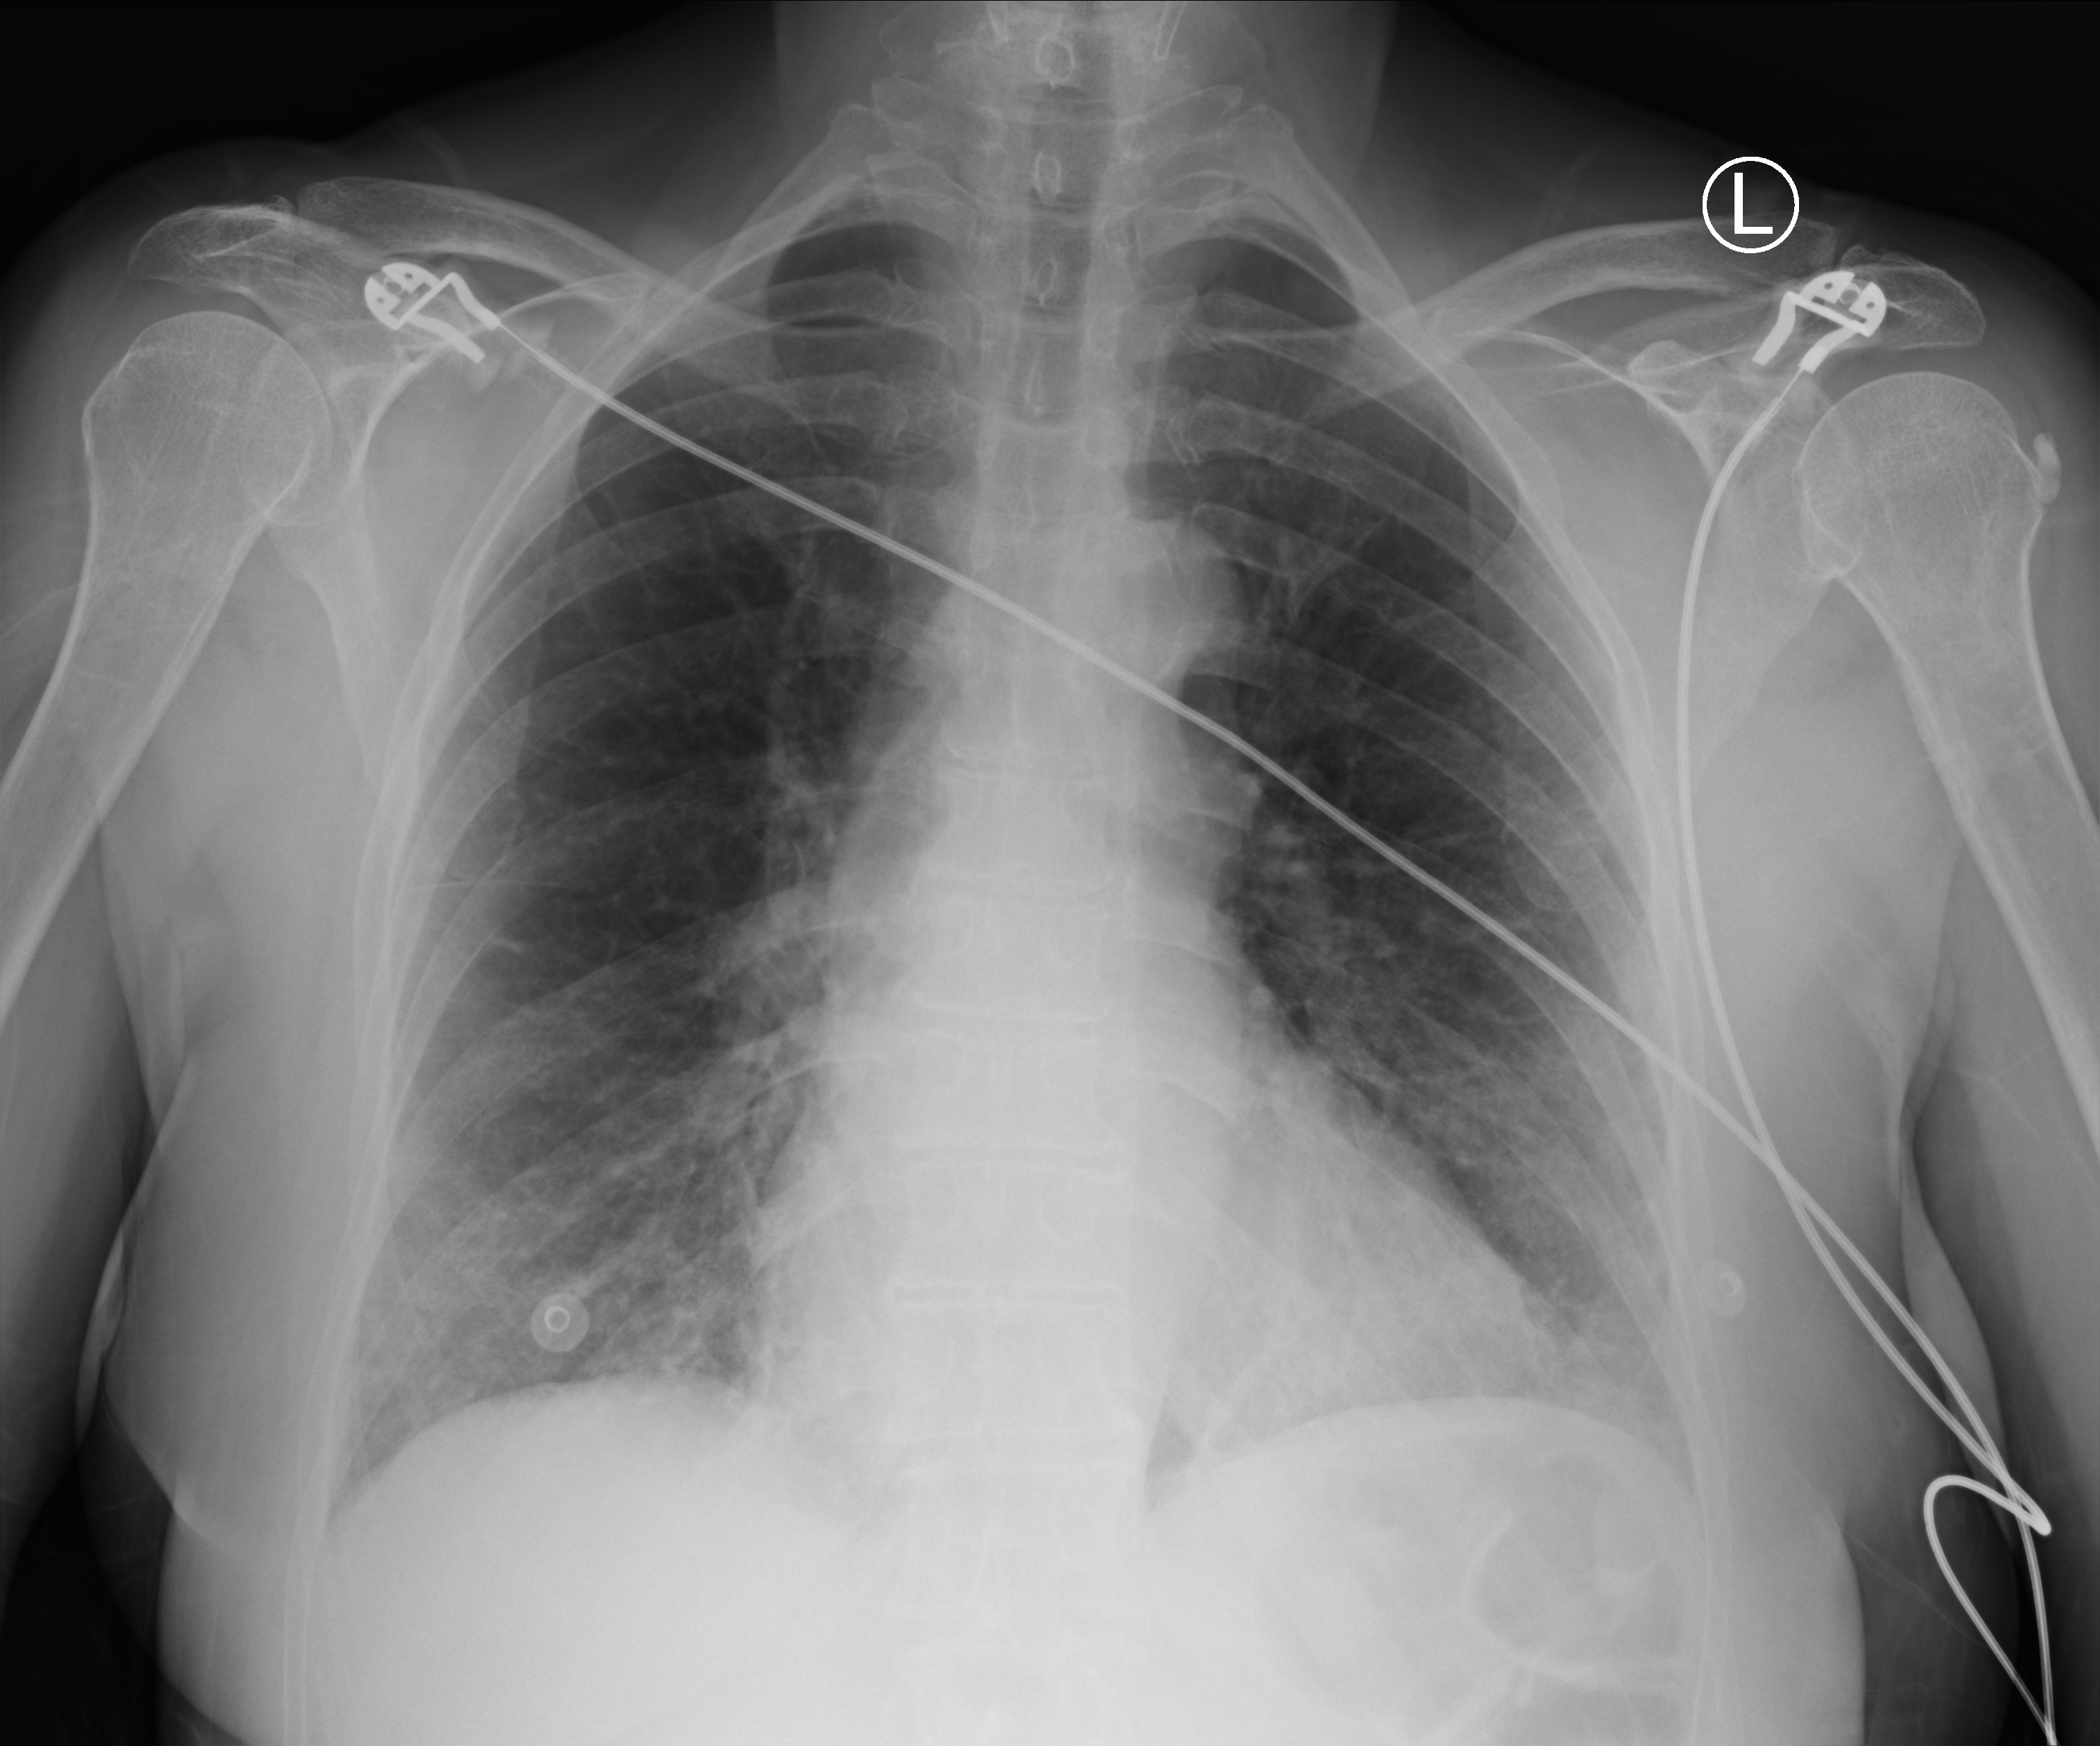
Chest X-ray (portable); anteroposterior (AP) projection. Female patient hospitalised with COVID-19, age 60–74 years.
Hospital-stay facts (about this admission, not read from this image; timing relative to this image not recorded): mechanically ventilated during this hospital stay: no; hypertension (admission record): no.